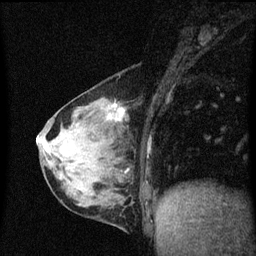
Breast MRI (dynamic contrast-enhanced), one sagittal slice. Slice 20 of 60 in the series (ordered by position). Dynamic contrast-enhanced series, image 2 of 3 at this slice position (ordered by acquisition). 1.5 T. TE 4.2 ms, TR 8.4 ms. 2 mm slice thickness. 256 × 256 image matrix, field of view 200 × 200 mm. Patient: female, 64 years. Case-level facts recorded for this patient, not image findings: setting: breast cancer imaged before/during neoadjuvant chemotherapy; receptor status: HR-positive, HER2-negative.
Structures marked on this image (semi-automatic segmentation, software-assisted and operator-edited):
- analysis volume of interest (the breast-tissue region the enhancement analysis was run in; not a lesion): bounding box <65,96,130,157> (left, top, right, bottom; pixels)
- tumour enhancement mask (voxels above the 70 % enhancement threshold inside the analysis volume of interest): <114,104,125,121>